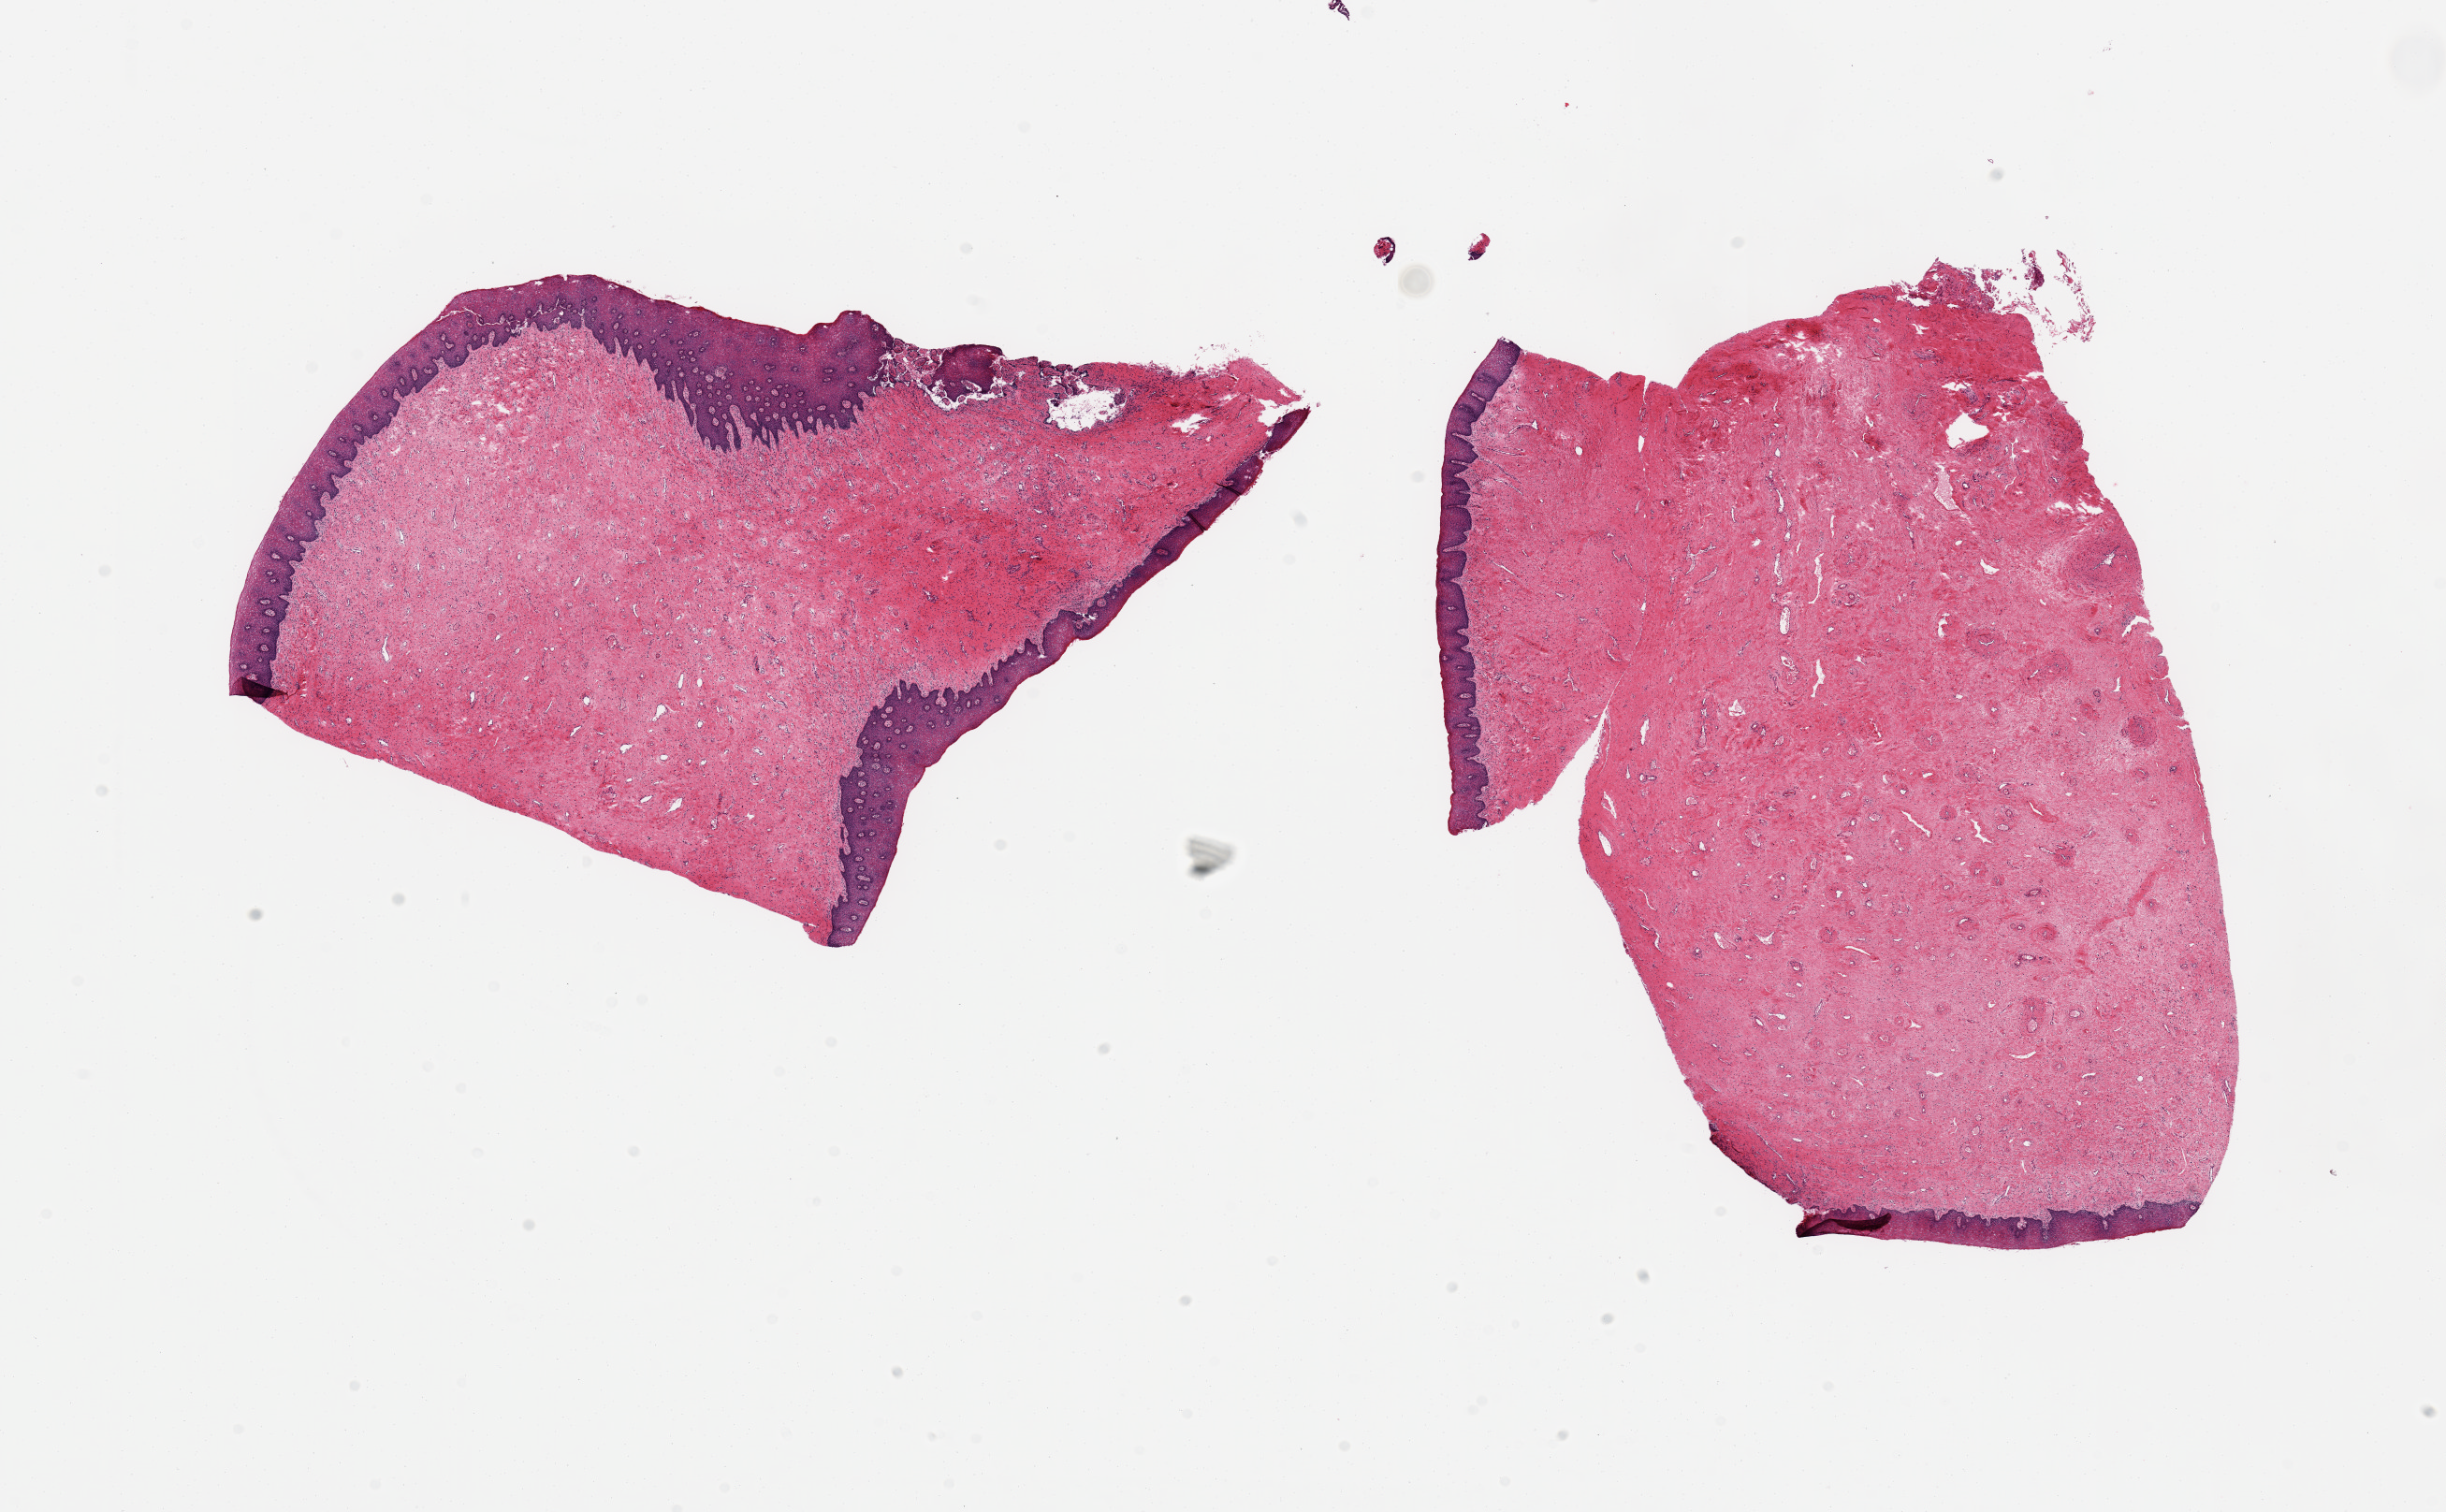
Whole-slide image, haematoxylin and eosin stain, brightfield, low-resolution overview of the scanned area, about 20.7 x 12.8 mm. PAXgene-fixed paraffin-embedded (PFPE) section. Section of exocervix (target tissue). Tissue donor sample. Donor sex: female.
• reviewer comment on this tissue sample: 2 ~ 5x5mm pieces. Squamous epithelium well preserved; in well-oriented areas ~4-5% of thickness